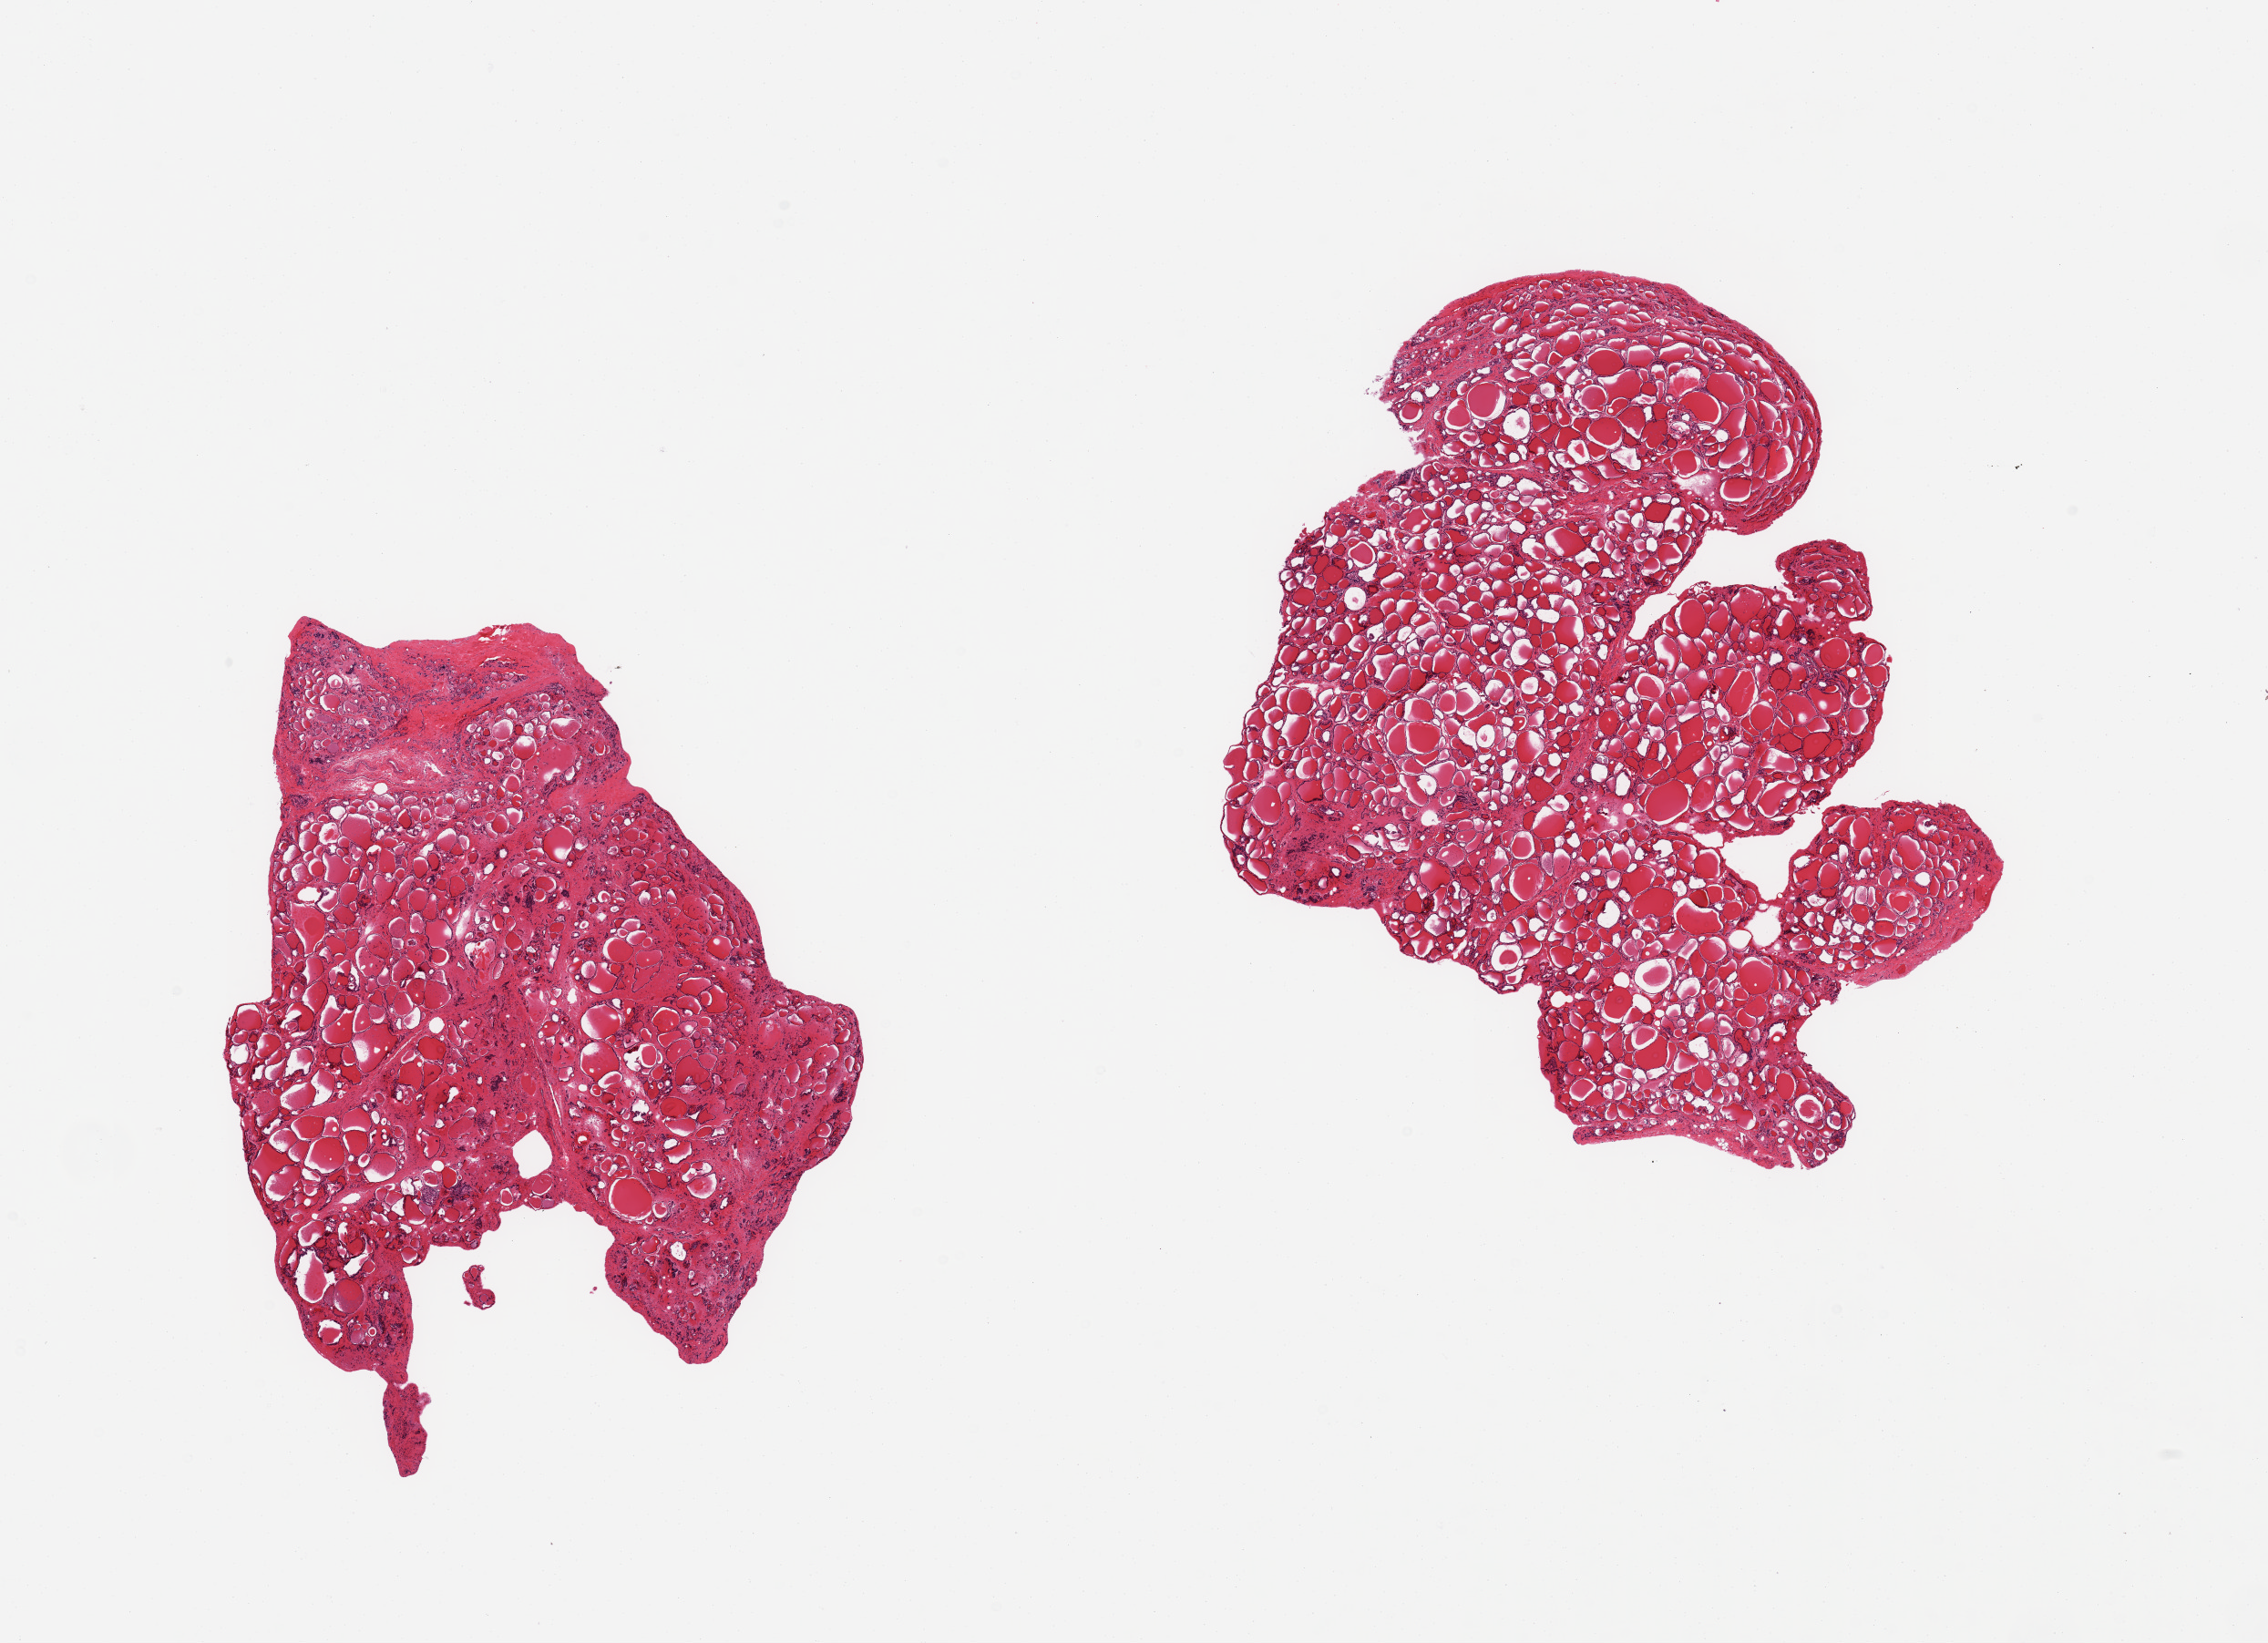
Digitized hematoxylin and eosin (H&E)-stained section — whole scanned area (about 19.7 x 14.3 mm) shown as a low-resolution overview, PAXgene-fixed paraffin-embedded (PFPE) section, sampled site (target tissue): thyroid, donor tissue sample.
- review note (as recorded): 2 pieces; fibrous septa and micronodularity